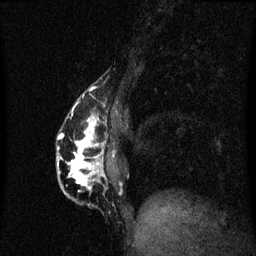
Breast MRI (dynamic contrast-enhanced), one sagittal slice; slice 18 of 60 in the series (ordered by position); dynamic contrast-enhanced series, image 2 of 3 at this slice position (ordered by acquisition); 1.5 T; TE 4.2 ms, TR 8.4 ms; 256 × 256 image matrix. Female patient, age 40 years.
Outlined on this slice (semi-automatically segmented with operator editing):
- analysis volume of interest (the breast-tissue region the enhancement analysis was run in; not a lesion): bounding box [x1, y1, x2, y2] px = [57, 84, 112, 207]
- tumour enhancement mask (voxels above the 70 % enhancement threshold inside the analysis volume of interest): [58, 106, 107, 191]